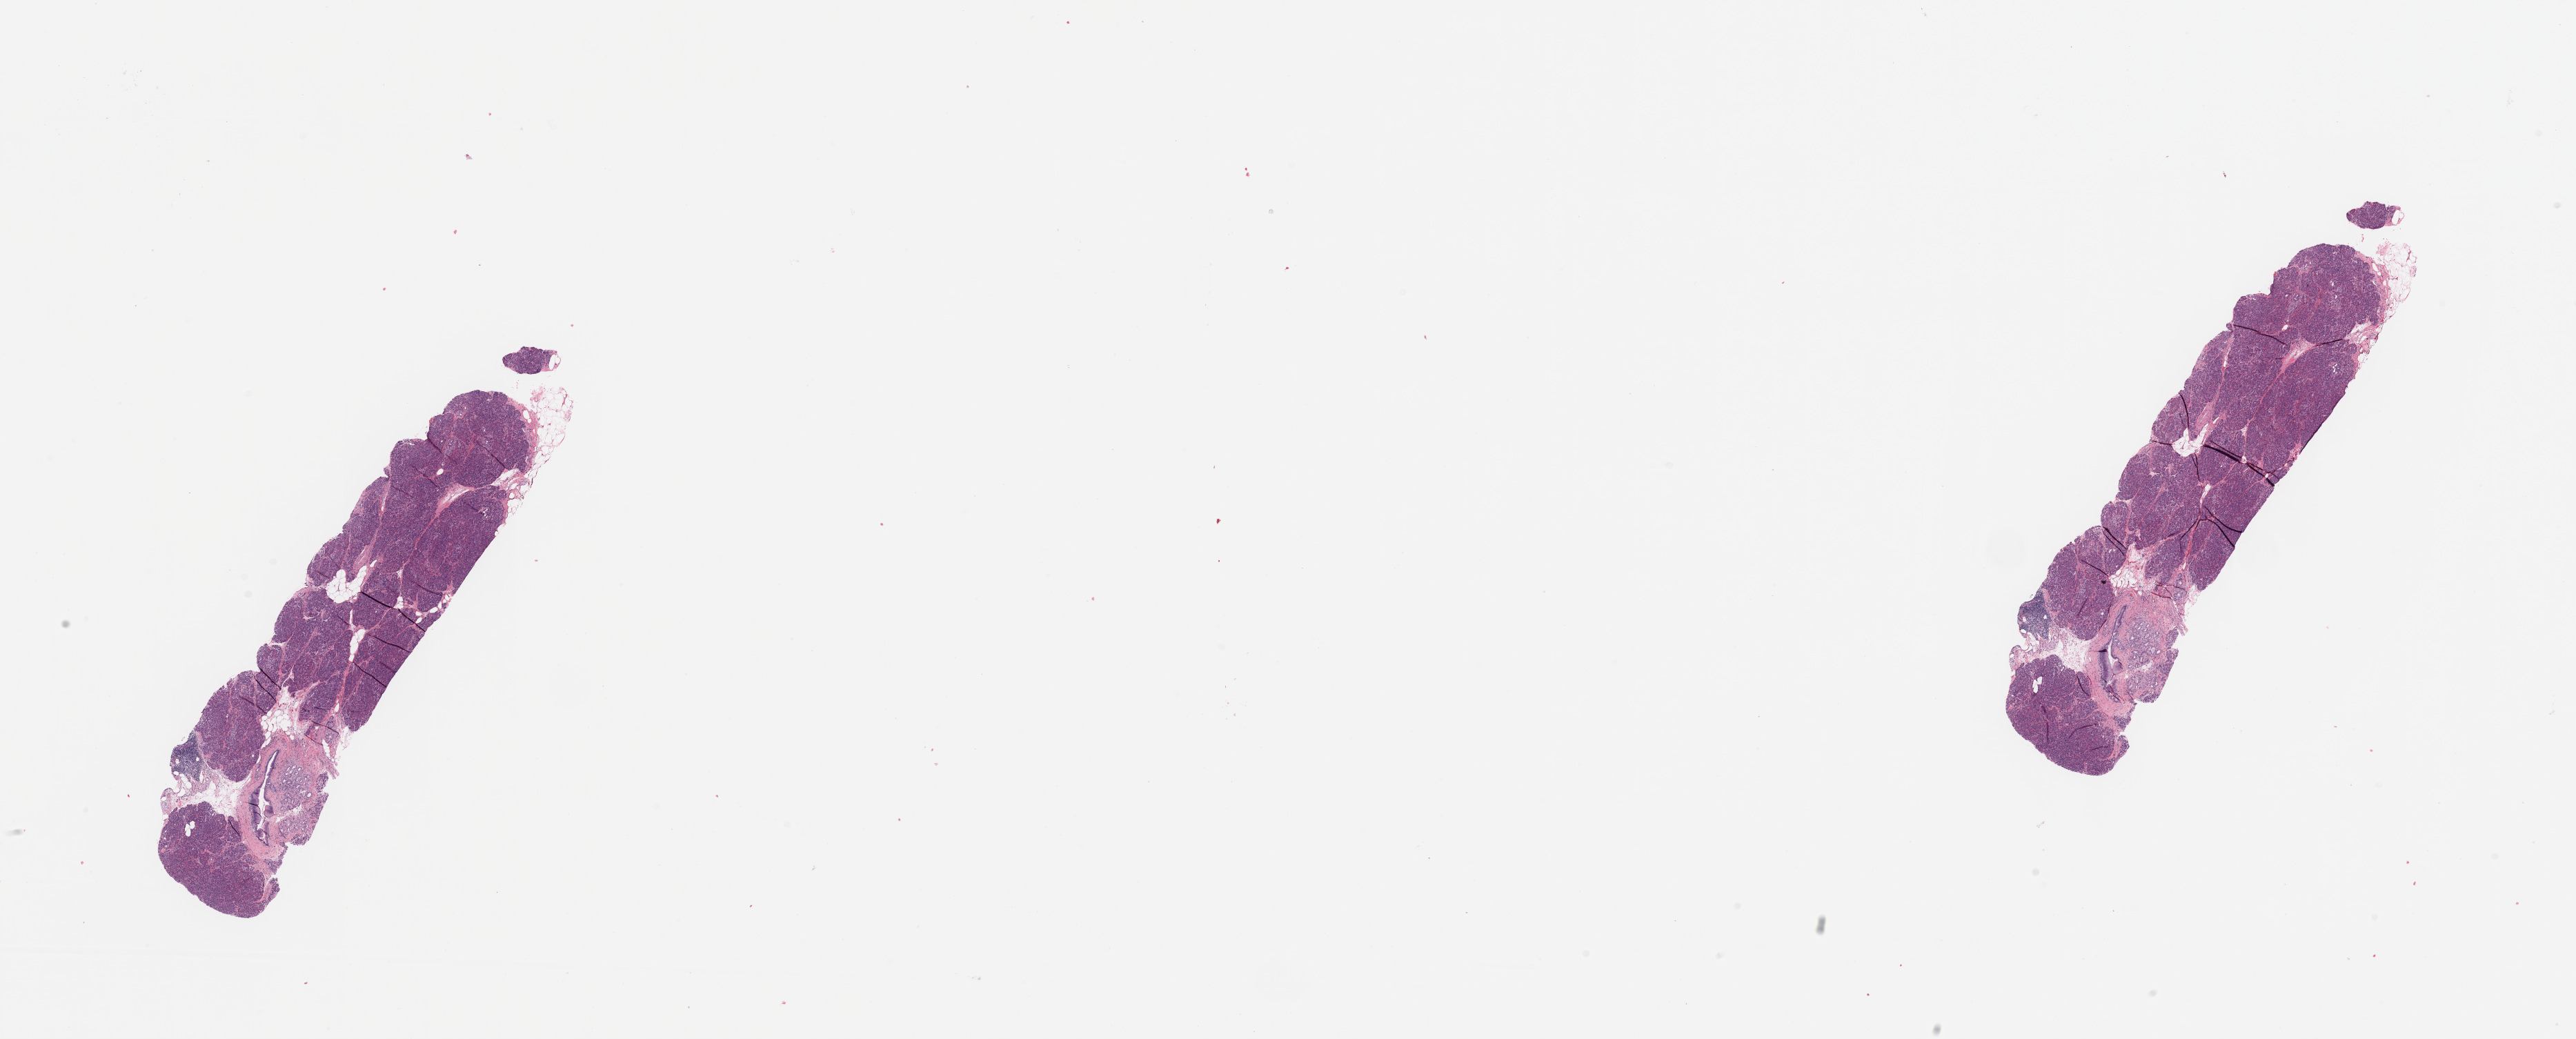
Hematoxylin and eosin (H&E) stained whole-slide image — shown as a low-resolution overview of the whole scanned area (about 29.5 x 11.9 mm, from a 20x scan), normal (non-tumour) tissue sample, sampled site: pancreas. Female, 60 y/o.
This section: normal (non-tumour) tissue from the same patient. Patient diagnosis: Infiltrating duct carcinoma, NOS.